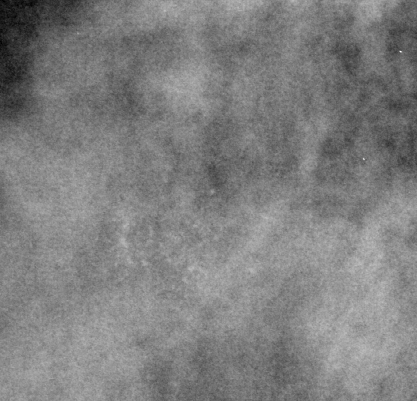
Crop from a digitized film mammogram around one marked abnormality, right breast, MLO view.
Calcifications, morphology amorphous, distribution clustered; BI-RADS assessment category 4; pathology (as recorded): benign.